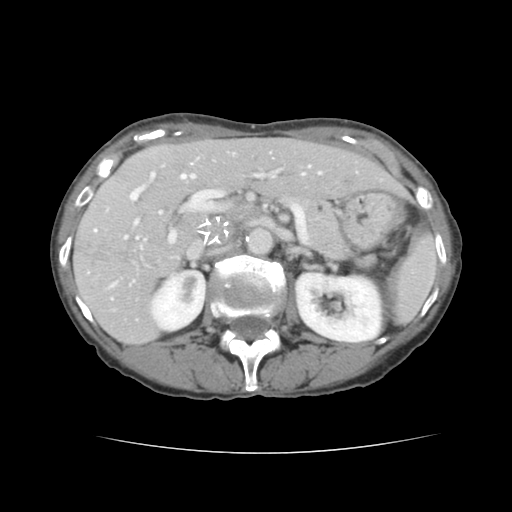
Contrast-enhanced abdominal CT, one axial slice. Slice 79 of 136 in the series (ordered by position). 120 kVp. Soft-tissue window (W 400 / L 40 HU). 512 × 512 image matrix, field of view 319 × 319 mm. Female patient, age 77 years. From the clinical record (not read from this slice): diagnosis: colorectal cancer liver metastases, imaged before liver resection; multiple liver metastases: yes; largest metastasis: 3 cm; disease in both lobes: no.
Structures marked on this image (manually delineated by an expert):
- hepatic veins: bounding box <136,166,321,239> (left, top, right, bottom; pixels)
- liver: <75,138,403,343>
- planned liver remnant (the part of the liver to remain after resection): <155,138,404,199>
- portal vein (with intrahepatic branches): <94,172,274,286>